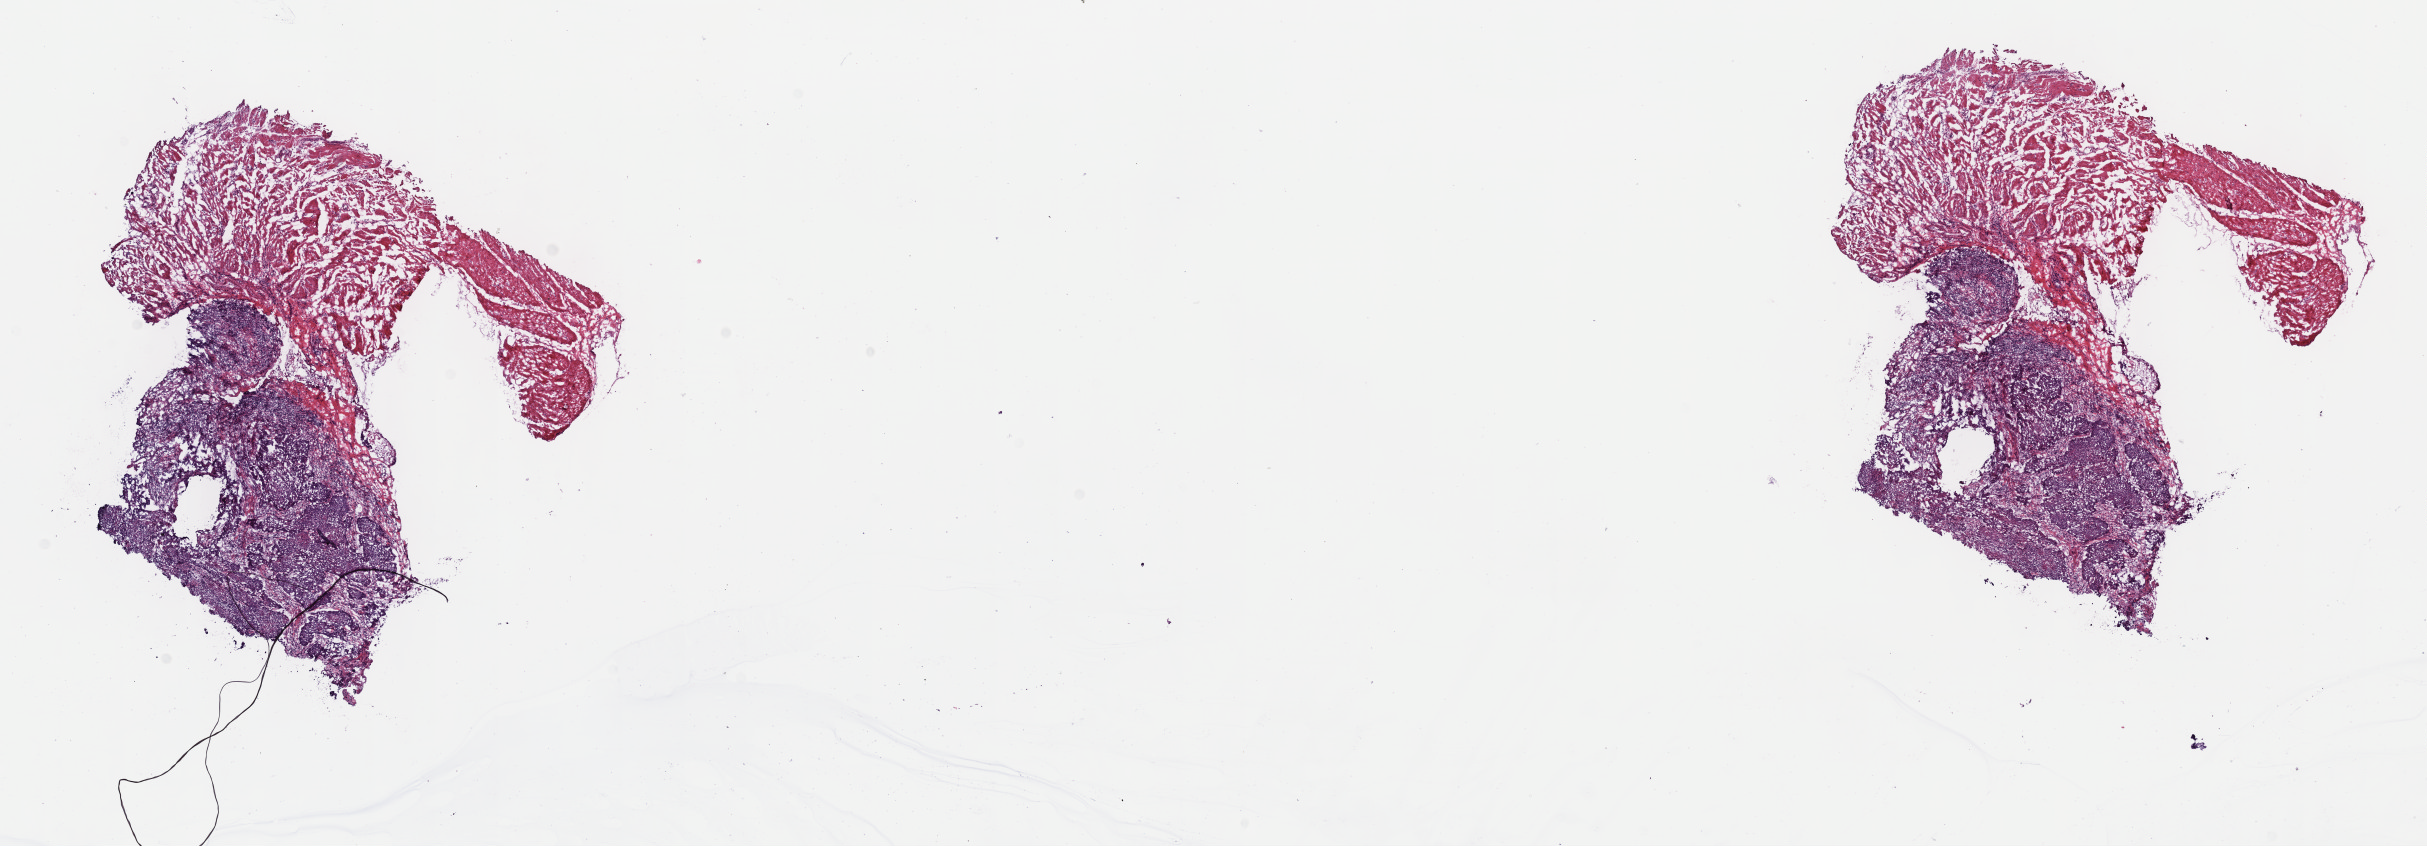
Whole-slide histology image, H&E, shown as a low-resolution overview of the whole scanned area (about 19.6 x 6.8 mm), frozen section from the top of the tissue portion, esophagus, primary tumour sample. Female, age 60 years at initial diagnosis. Histologic grade: G3 (poorly differentiated). Slide review estimates, as recorded: tumour cells 65%, tumour nuclei 65%, normal cells 0%, stromal cells 35%, necrosis 0%. Infiltration values recorded for this section: lymphocyte infiltration 10%, monocyte infiltration 0%, neutrophil infiltration 0%.
Pathologic diagnosis: Squamous cell carcinoma, NOS (middle third of esophagus). TNM: T2 N0 M0. AJCC pathologic stage: IIA.